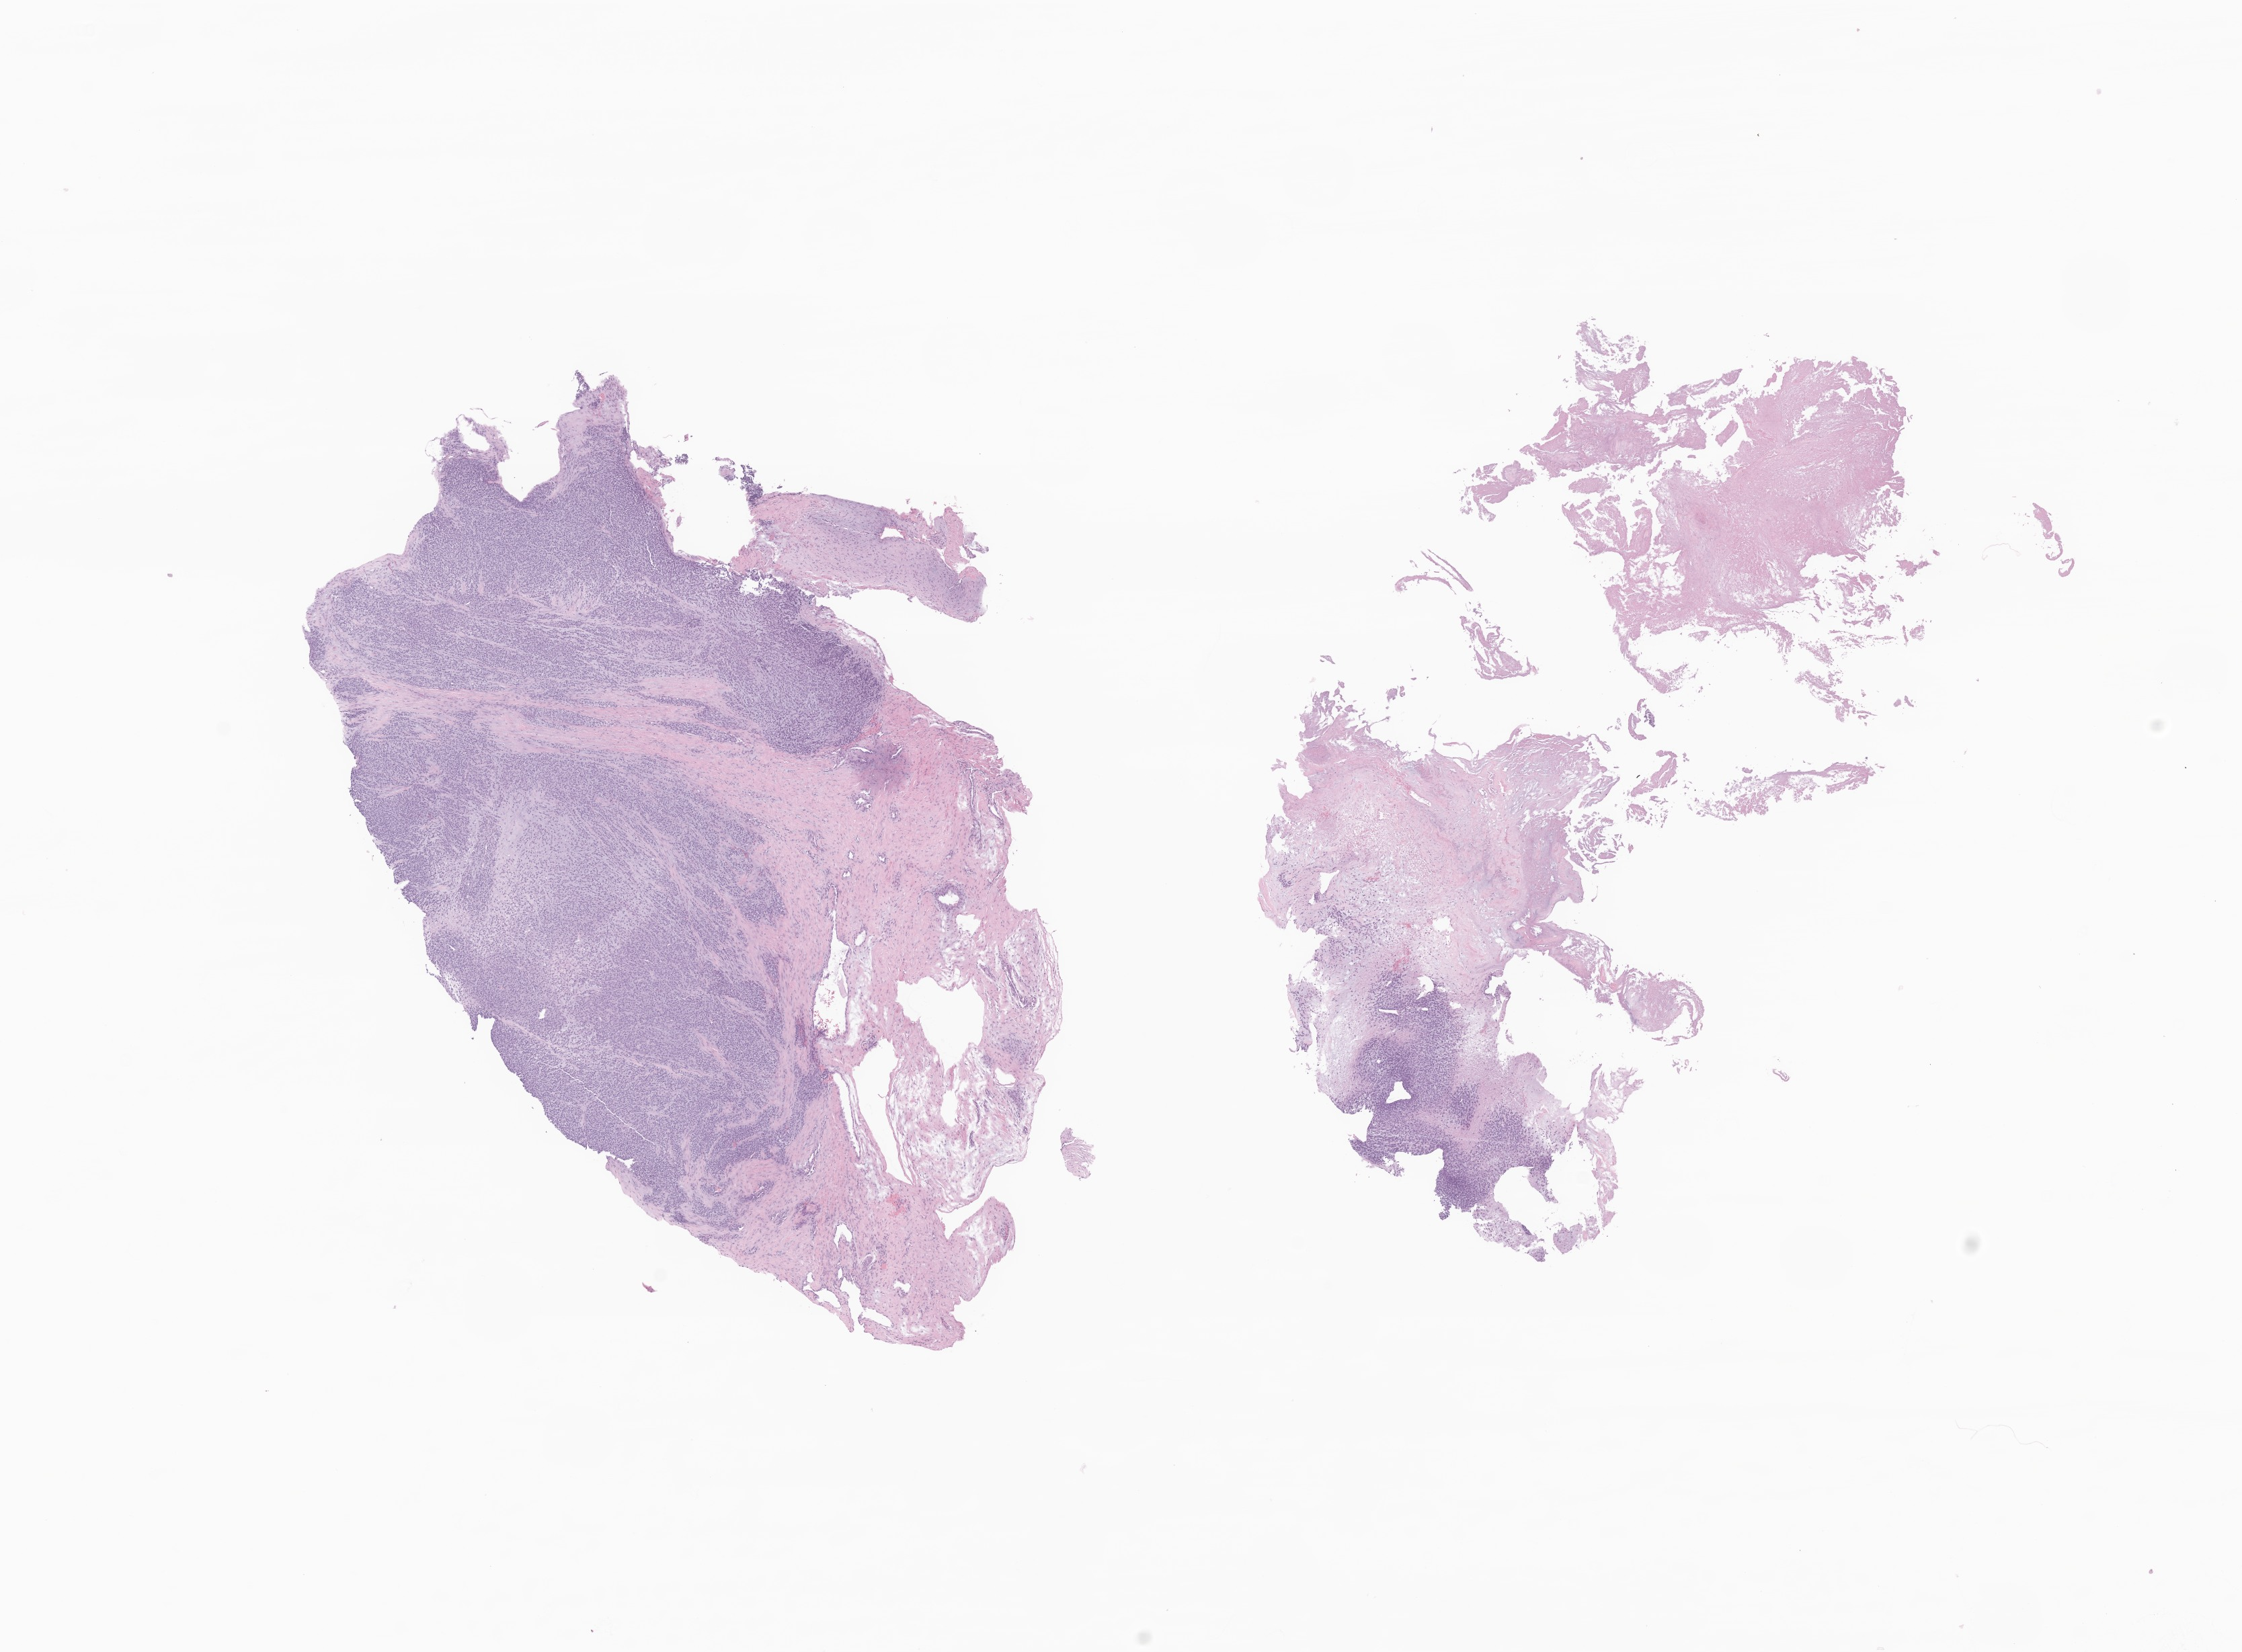
Hematoxylin and eosin (H&E) whole-slide image of tumor tissue from the soft tissue of abdomen, shown as a low-resolution overview of the whole scanned area (about 14.1 x 10.4 mm), formalin-fixed paraffin-embedded section. Patient female; age 200 months (16 years 8 months).
Diagnosis (ICD-O-3 morphology term): Sarcoma, NOS.